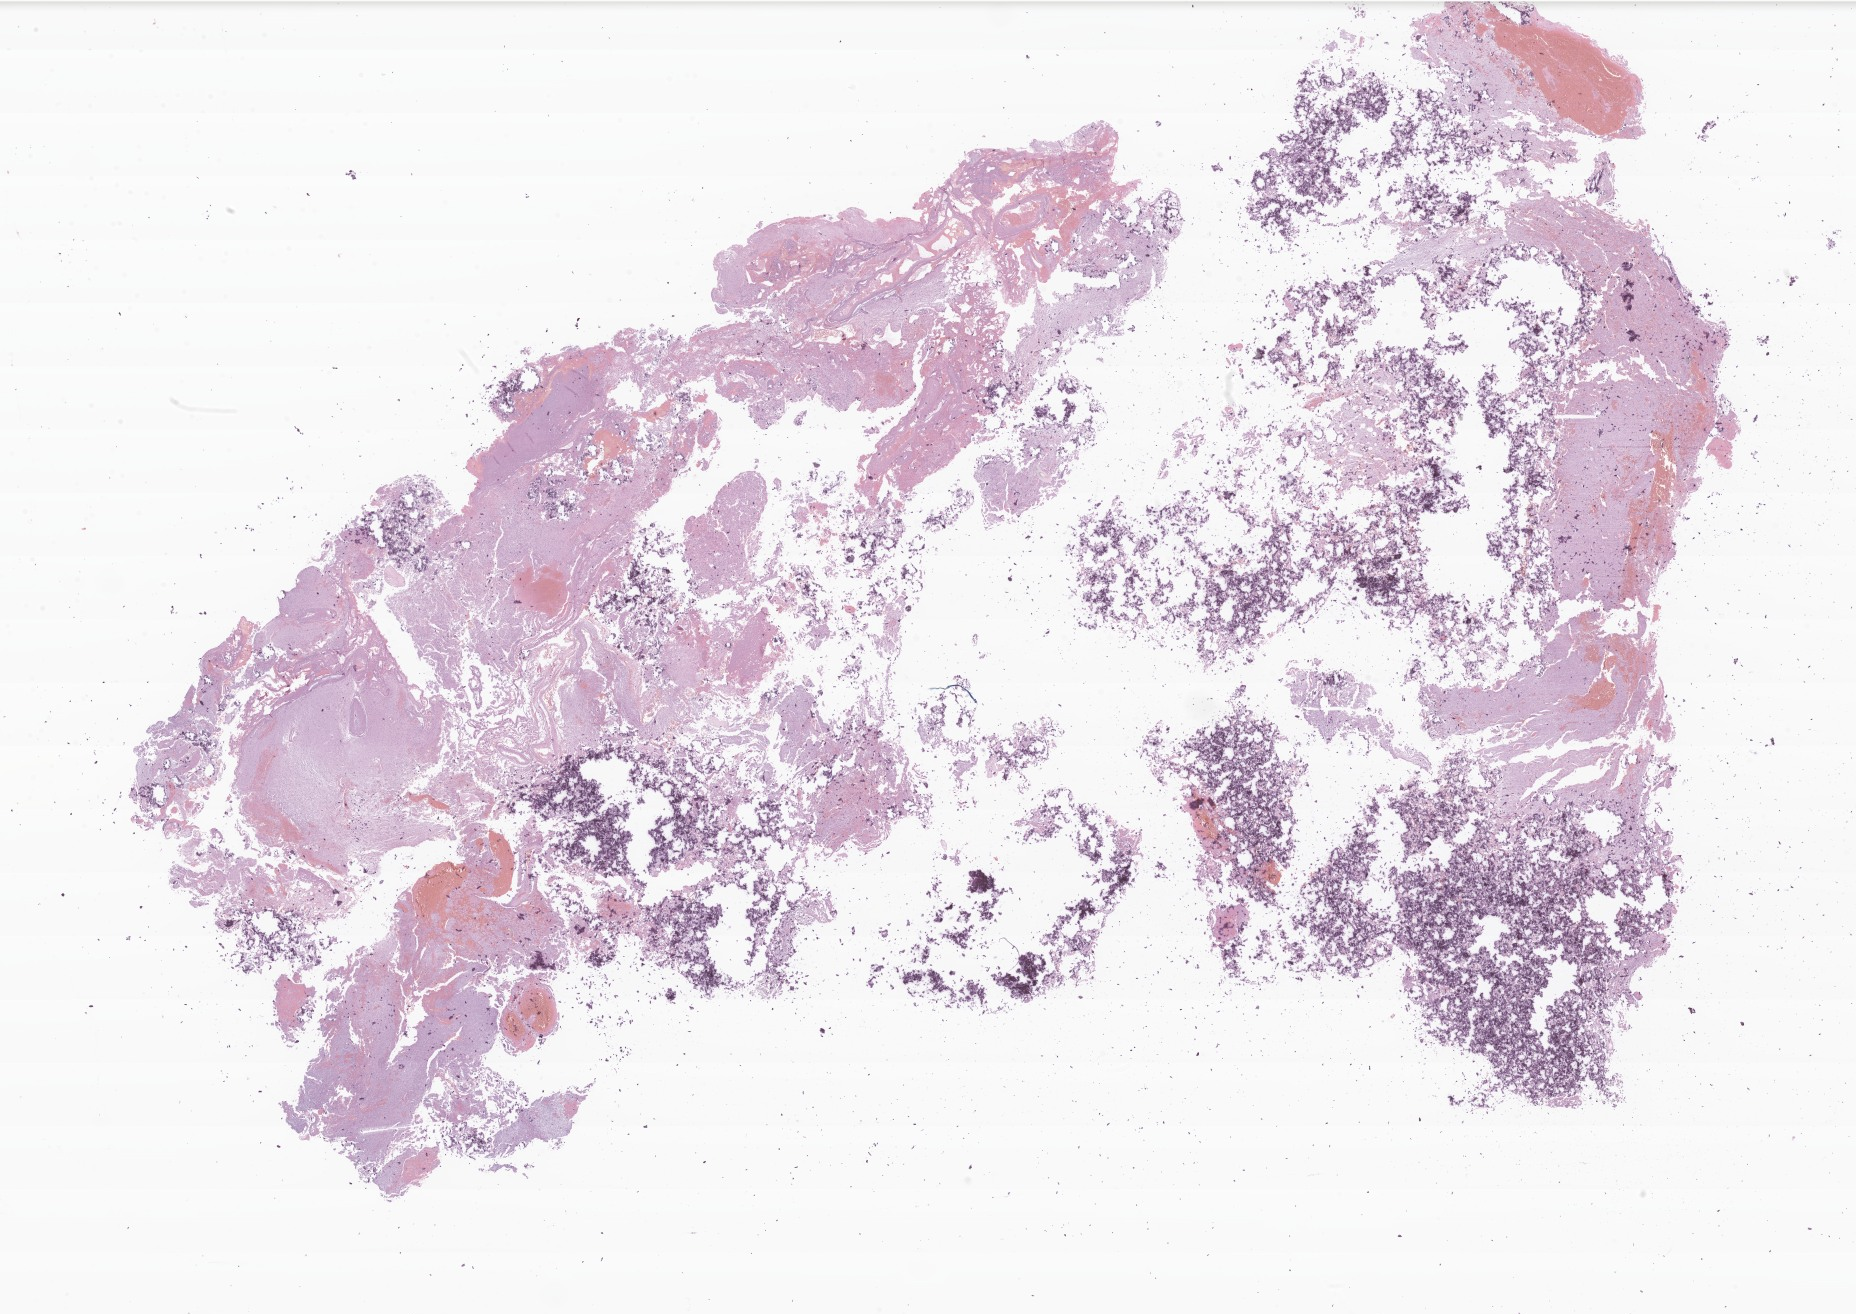
Whole-slide image, H&E stain of tumor tissue from the brain, a low-resolution overview of the entire scanned area, about 31.2 x 22.1 mm; formalin-fixed, paraffin-embedded (FFPE) tissue. Patient male; age 214 months (17 years 10 months).
- recorded diagnosis: Ganglioglioma, NOS